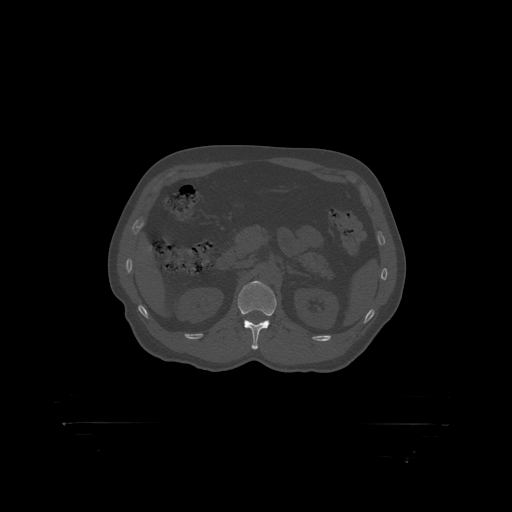
CT including the spine, one axial slice; slice 322 of 399 in the series (ordered by position); reconstruction kernel STANDARD; 120 kVp; bone window (W 1800 / L 400 HU); 1.25 mm slice thickness; 512 × 512 image matrix, field of view 650 × 650 mm. Male patient, age 46 years. From the clinical record (not read from this slice): primary cancer: skin.
Structures marked on this image (semi-automatic segmentation, software-assisted and operator-edited):
- L1 vertebra: box from (x=238, y=282) to (x=277, y=317) px